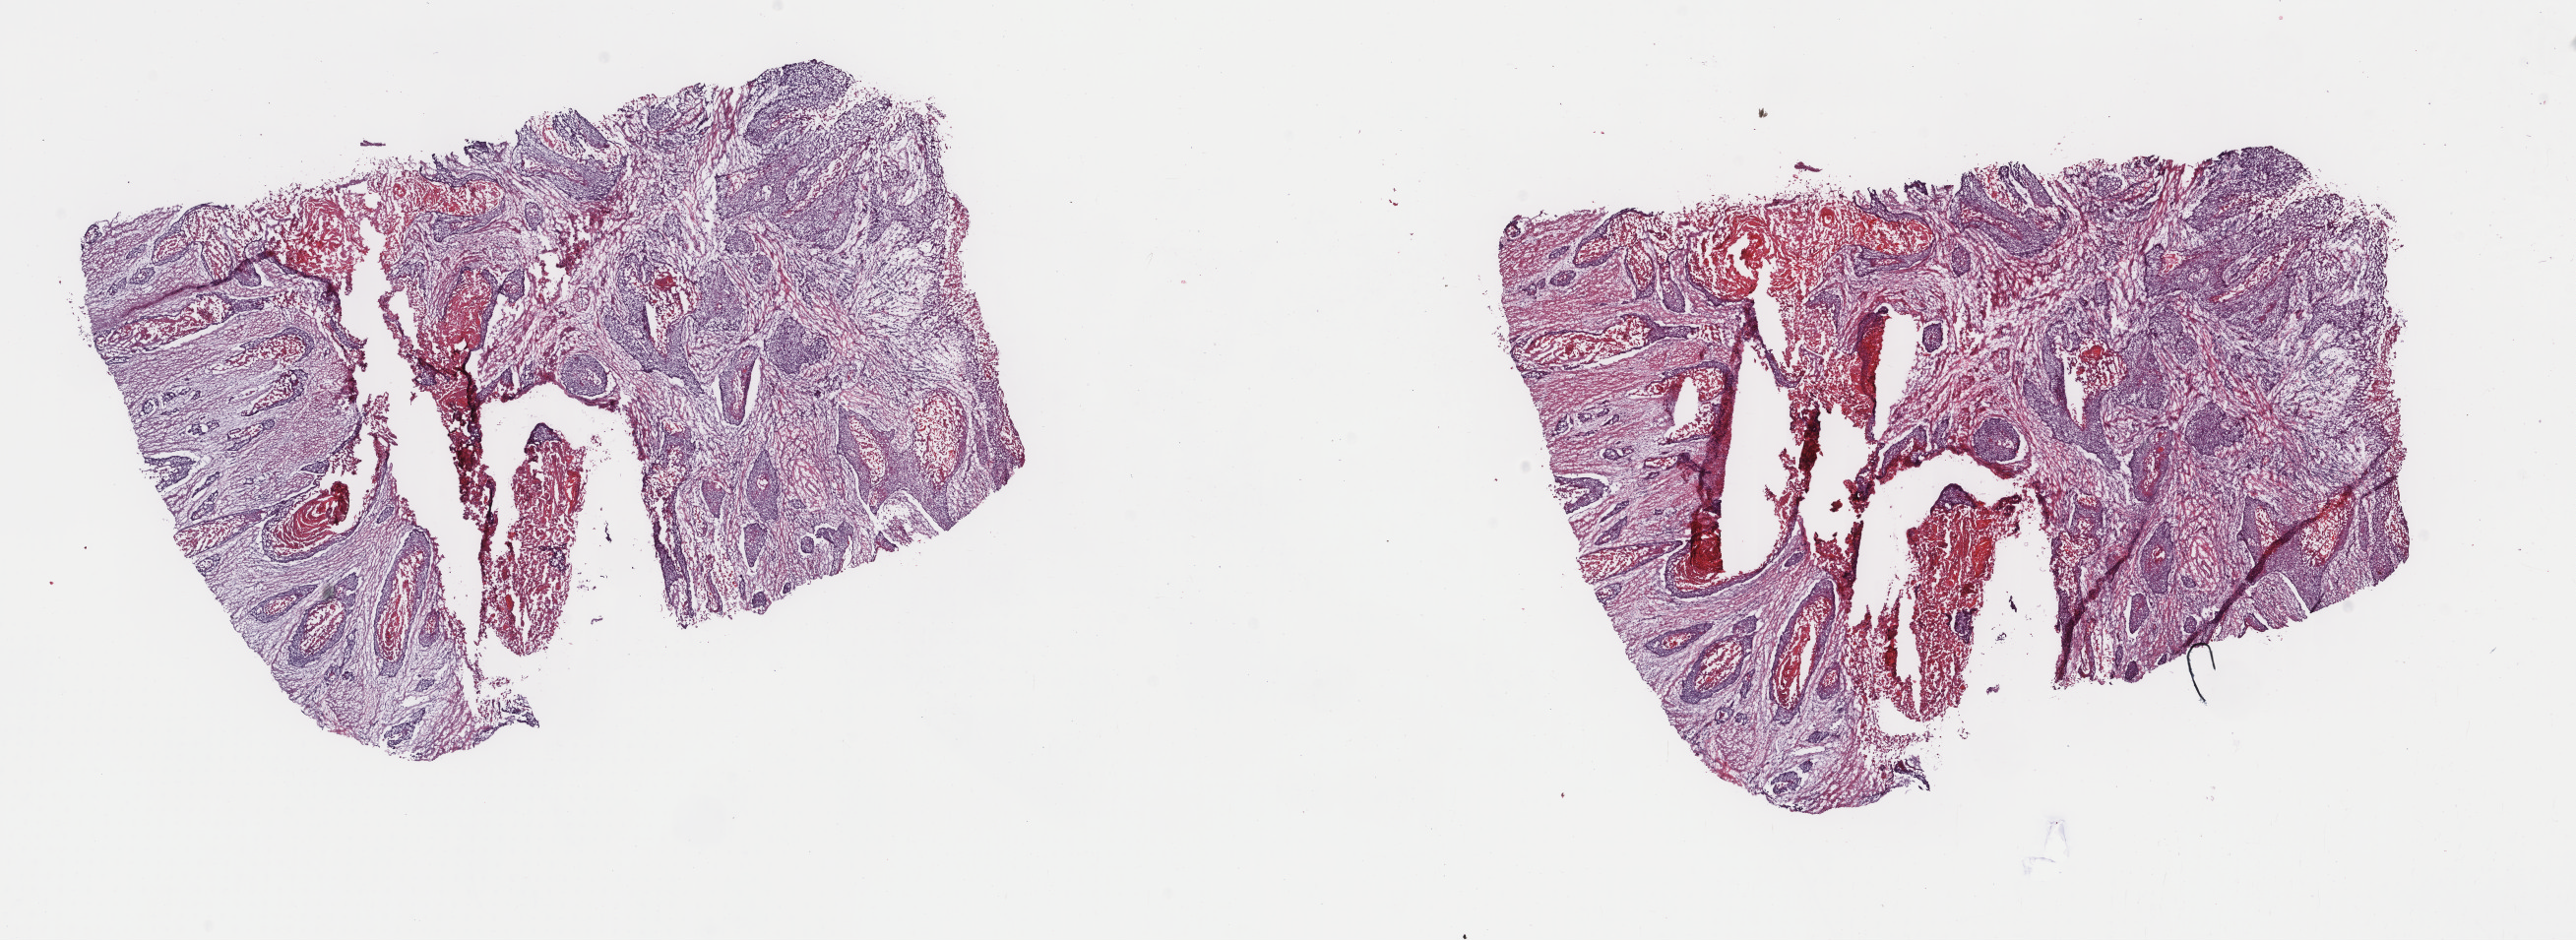
H&E-stained whole-slide image — low-resolution overview of the scanned area, about 20.8 x 7.6 mm (slide scanned at 40x). Frozen section from the top of the tissue portion. Primary tumour sample from the esophagus. Male, age 36 years at initial diagnosis. Histologic grade: GX (grade cannot be assessed). Composition of this section per pathologist review: tumour cells 85%, tumour nuclei 70%, normal cells 0%, stromal cells 0%, necrosis 15%. Inflammatory infiltration, as recorded: lymphocyte infiltration 0%, monocyte infiltration 0%, neutrophil infiltration 0%.
* histologic diagnosis: Squamous cell carcinoma, NOS (lower third of esophagus)
* AJCC pathologic stage: III